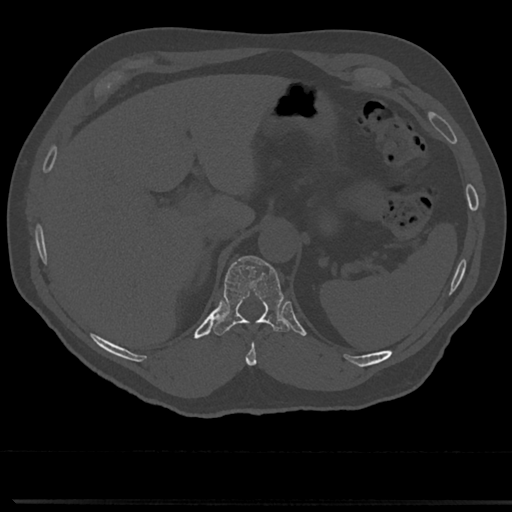
CT including the spine, one axial slice. Position 214 of 817 along the scan axis. Reconstruction kernel Br40s/3. 120 kVp. Bone window (W 1800 / L 400 HU). 0.5 mm slice thickness. 512 × 512 image matrix. Male patient, age 61 years. From the clinical record (not read from this slice): primary cancer: prostate.
Outlined on this slice (semi-automatically segmented with operator editing):
- T10 vertebra: box from (x=246, y=327) to (x=262, y=366) px
- T11 vertebra: (x=215, y=256)–(x=288, y=335)